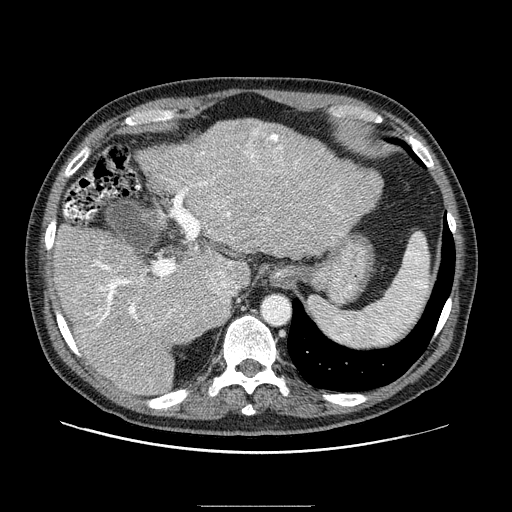
Contrast-enhanced abdominal CT (liver protocol), one axial slice. Slice 61 of 99 in the series (ordered by position). 100 kVp. One of 2 acquisitions stored at this slice position. Soft-tissue window (W 400 / L 40 HU). 512 × 512 image matrix, field of view 400 × 400 mm. From the clinical record (not read from this slice): diagnosis: hepatocellular carcinoma (patient treated with transarterial chemoembolisation; whether this scan precedes or follows treatment is not stated here); TNM stage (as recorded): Stage-II; Child-Pugh class: A; tumour differentiation: well differentiated.
Structures marked on this image (semi-automatic segmentation, software-assisted and operator-edited):
- abdominal aorta: bounding box (x1, y1, x2, y2) in pixels: (263, 296, 291, 324)
- liver parenchyma outside the tumour (the mass and vessels are separate outlines, so this box may not span the whole liver): (54, 119, 382, 394)
- mass: (245, 127, 285, 173)
- liver vessels: (74, 146, 340, 377)